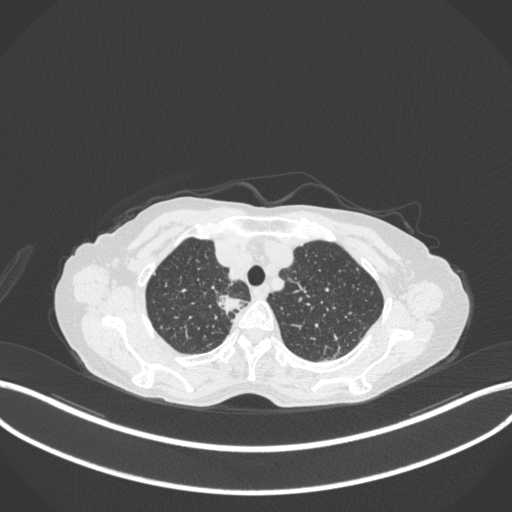
Chest CT, one axial slice. Position 310 of 363 along the scan axis. Reconstruction kernel B31f. 120 kVp. Lung window (W 1500 / L -600 HU). 512 × 512 image matrix, field of view 400 × 400 mm. Female patient, age 75 years. Case-level facts recorded for this patient, not image findings: clinical TNM (as recorded): T1c N1 M1.
Outlined on this slice (bounding box drawn by a radiologist):
- lung tumour (recorded histology: adenocarcinoma): bounding box <212,290,244,315> (left, top, right, bottom; pixels)